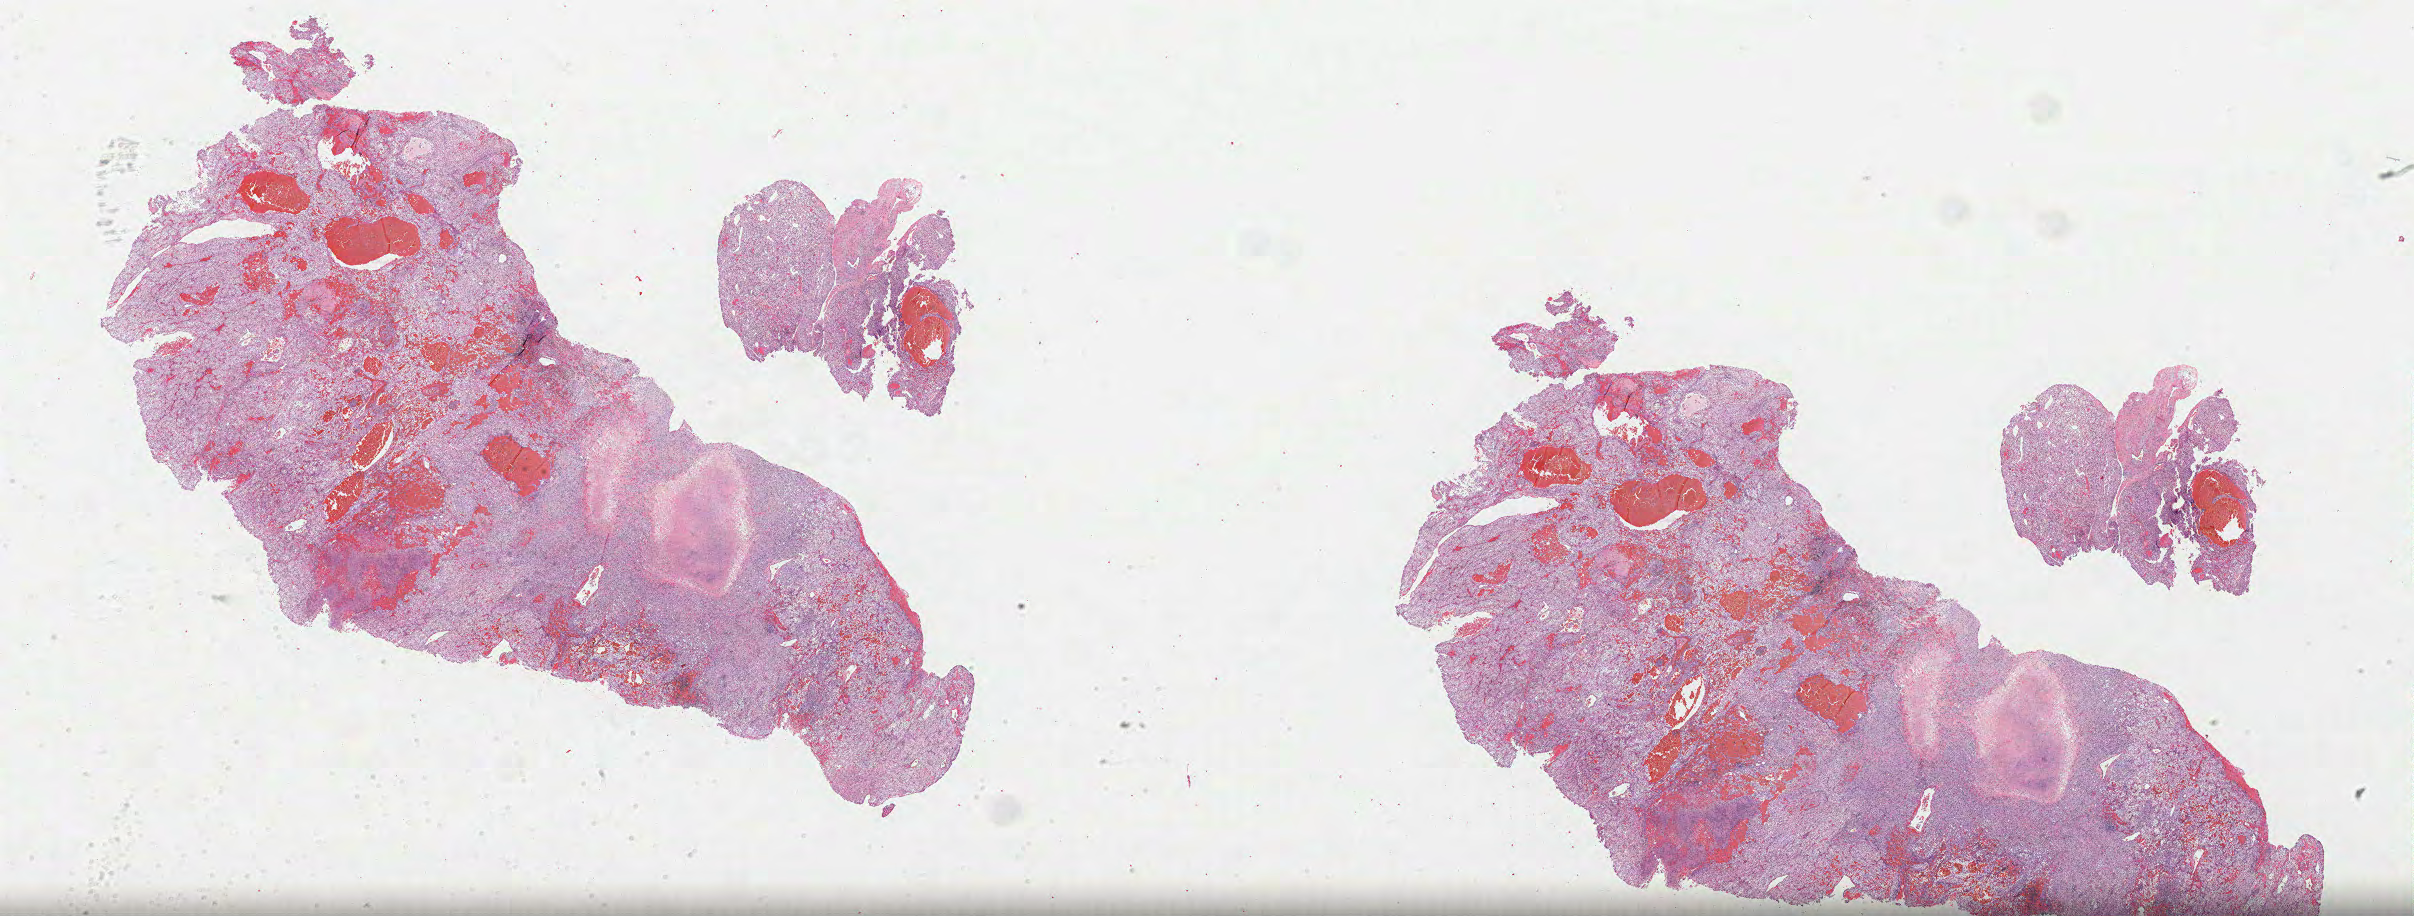
Whole-slide histology image, H&E-stained — low-resolution overview of the scanned area, about 38.9 x 14.8 mm (from a 40x scan), formalin-fixed paraffin-embedded (FFPE) diagnostic section, sample: primary tumour, kidney. Male, age 83 years at initial diagnosis.
Pathologic diagnosis: Clear cell adenocarcinoma, NOS.